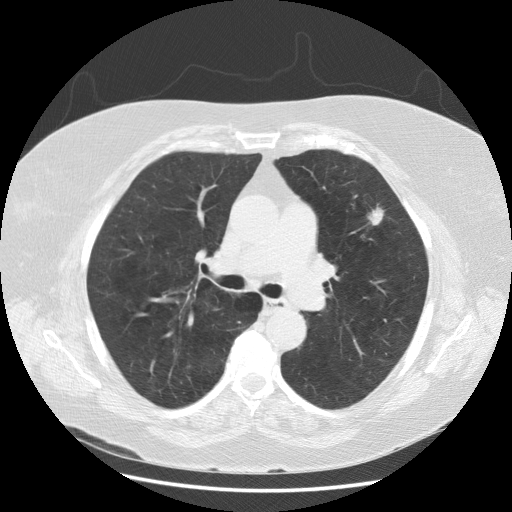
Low-dose screening chest CT, one axial slice. Position 101 of 164 along the scan axis. 120 kVp. Lung window (W 1500 / L -600 HU). 2.5 mm slice thickness. 512 × 512 image matrix, field of view 380 × 380 mm.
Outlined on this slice (expert manual segmentation):
- lesion 1 (tumor, upper lobe of left lung): bounding box [x1, y1, x2, y2] px = [368, 205, 384, 226]